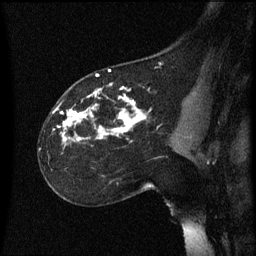
Breast MRI (dynamic contrast-enhanced), one sagittal slice; position 37 of 60 along the scan axis; dynamic contrast-enhanced series, image 2 of 3 at this slice position (ordered by acquisition); 1.5 T; TE 4.2 ms, TR 8.4 ms; 2.2 mm slice thickness; 256 × 256 image matrix, field of view 200 × 200 mm. Patient: female, 35 years. Case-level facts recorded for this patient, not image findings: setting: breast cancer imaged before/during neoadjuvant chemotherapy; receptor status: HER2-positive.
Outlined on this slice (semi-automatic segmentation, software-assisted and operator-edited):
- analysis volume of interest (the breast-tissue region the enhancement analysis was run in; not a lesion): bounding box [x1, y1, x2, y2] px = [39, 72, 178, 173]
- tumour enhancement mask (voxels above the 70 % enhancement threshold inside the analysis volume of interest): [54, 84, 151, 141]